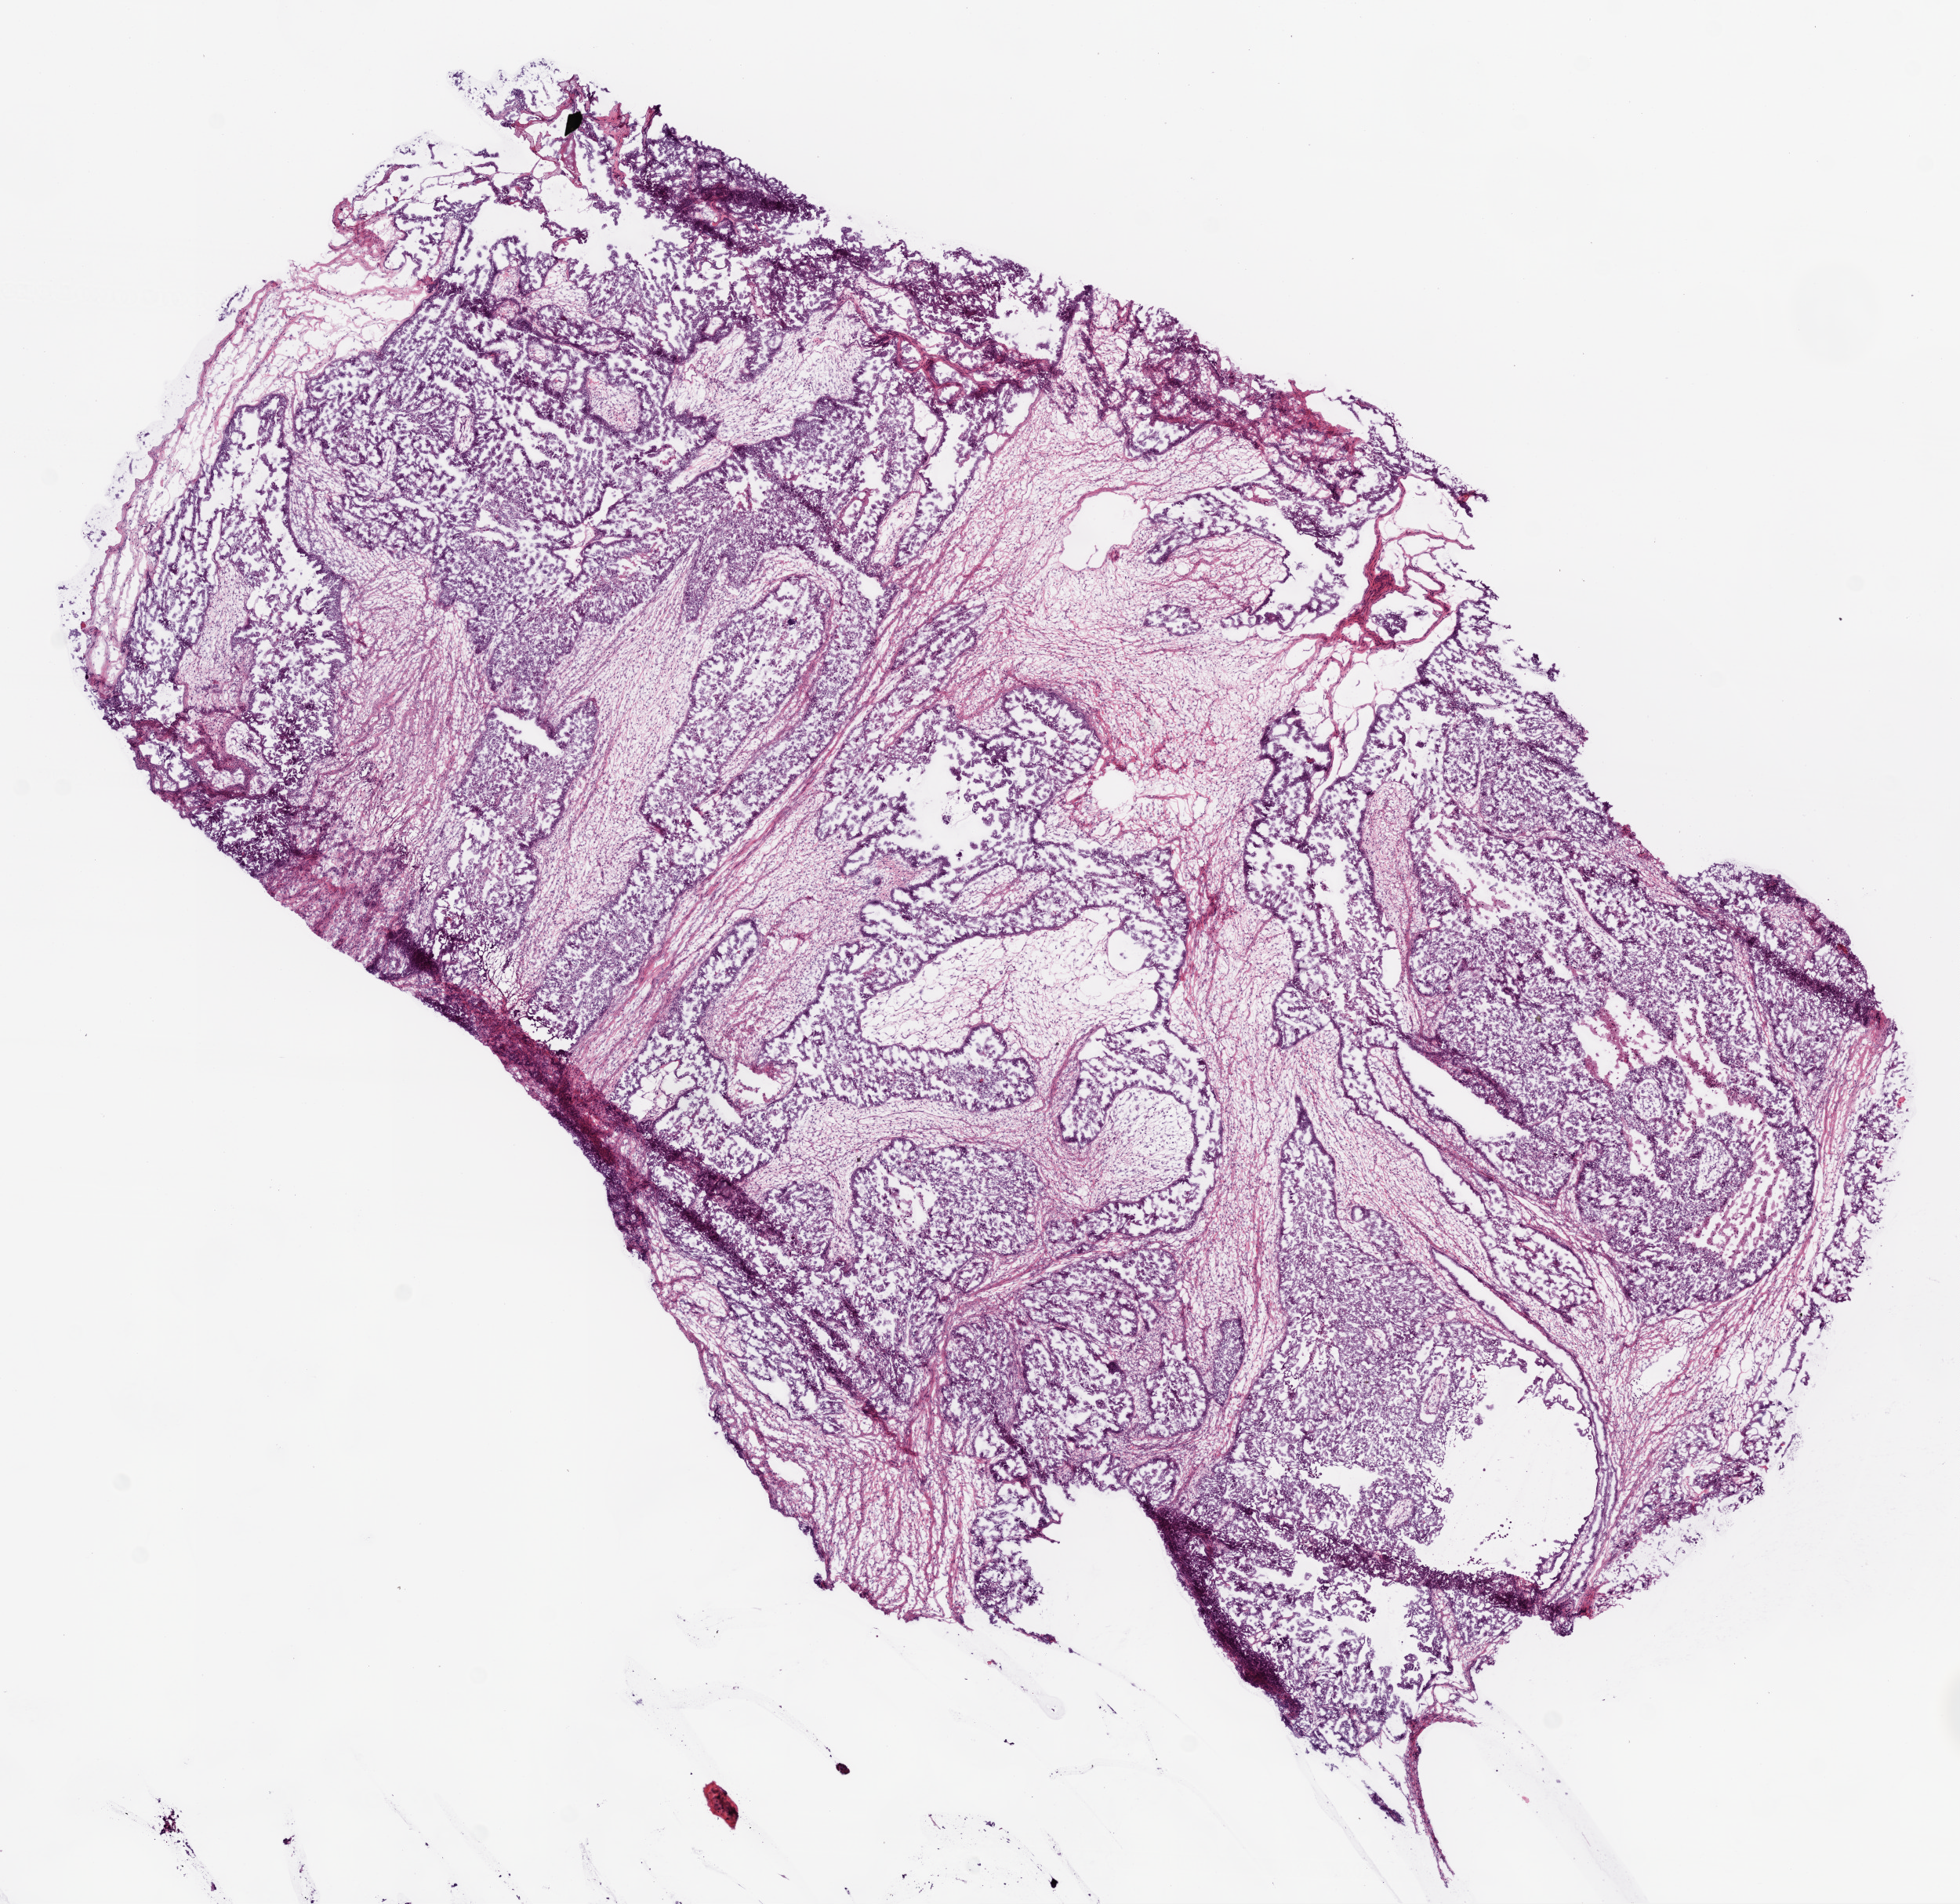
Digitized H&E tissue section (whole slide) — shown as a low-resolution overview of the whole scanned area (about 10.0 x 9.7 mm, from a 20x scan), frozen section from the bottom of the tissue portion, ovary, primary tumour sample. Female patient; age at initial diagnosis 46 years. Slide review estimates, as recorded: tumour cells 75%, tumour nuclei 80%.
Diagnosis: Serous cystadenocarcinoma, NOS.